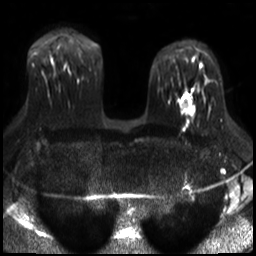
Breast MRI, one axial slice; position 19 of 30 along the scan axis; diffusion-weighted series; image 2 of 4 stored at this slice position (different b-values; order by instance number); 3 T; 256 × 256 image matrix, field of view 320 × 320 mm. Female patient.
Outlined on this slice (manually delineated by an expert):
- tumour on diffusion-weighted imaging: bounding box [x1, y1, x2, y2] px = [180, 102, 184, 108]